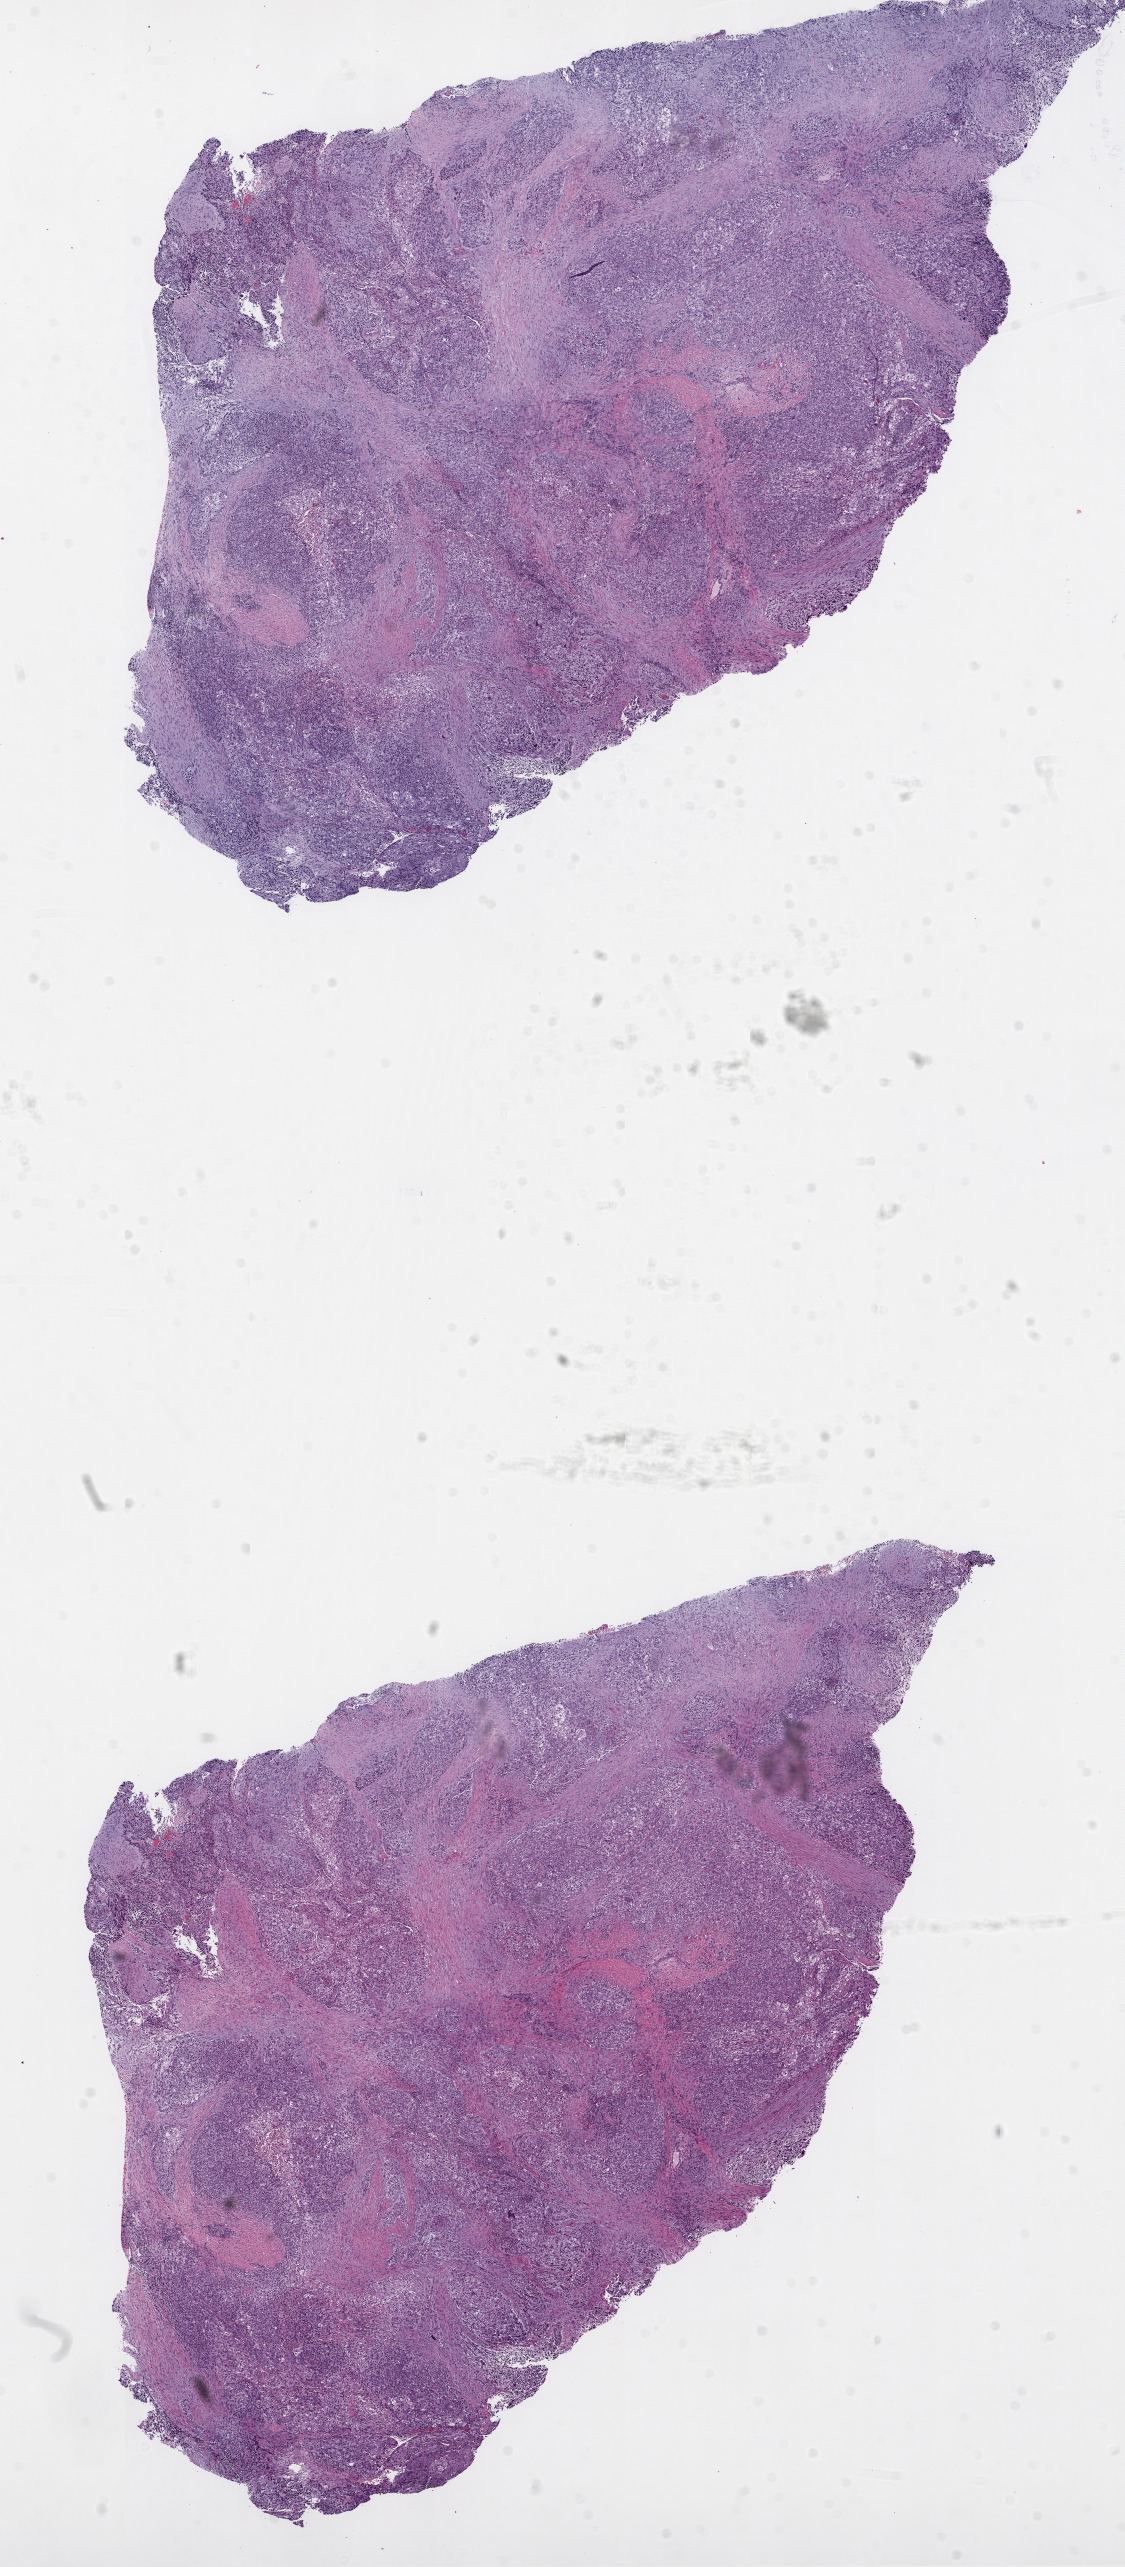
Digitized H&E tissue section (whole slide) — low-resolution overview of the scanned area, about 9.0 x 20.6 mm (acquisition: 20x scan), frozen section from the top of the tissue portion, lung, primary tumour sample. Patient: male, age at initial diagnosis 71 years. Composition of this section per pathologist review: tumour cells 80%, tumour nuclei 80%, normal cells 0%, stromal cells 18%, necrosis 2%. Inflammatory infiltration, as recorded: lymphocyte infiltration 10%.
AJCC pathologic stage: IB. TNM: T2 N0 M0. Pathologic diagnosis: Squamous cell carcinoma, NOS (upper lobe, lung).